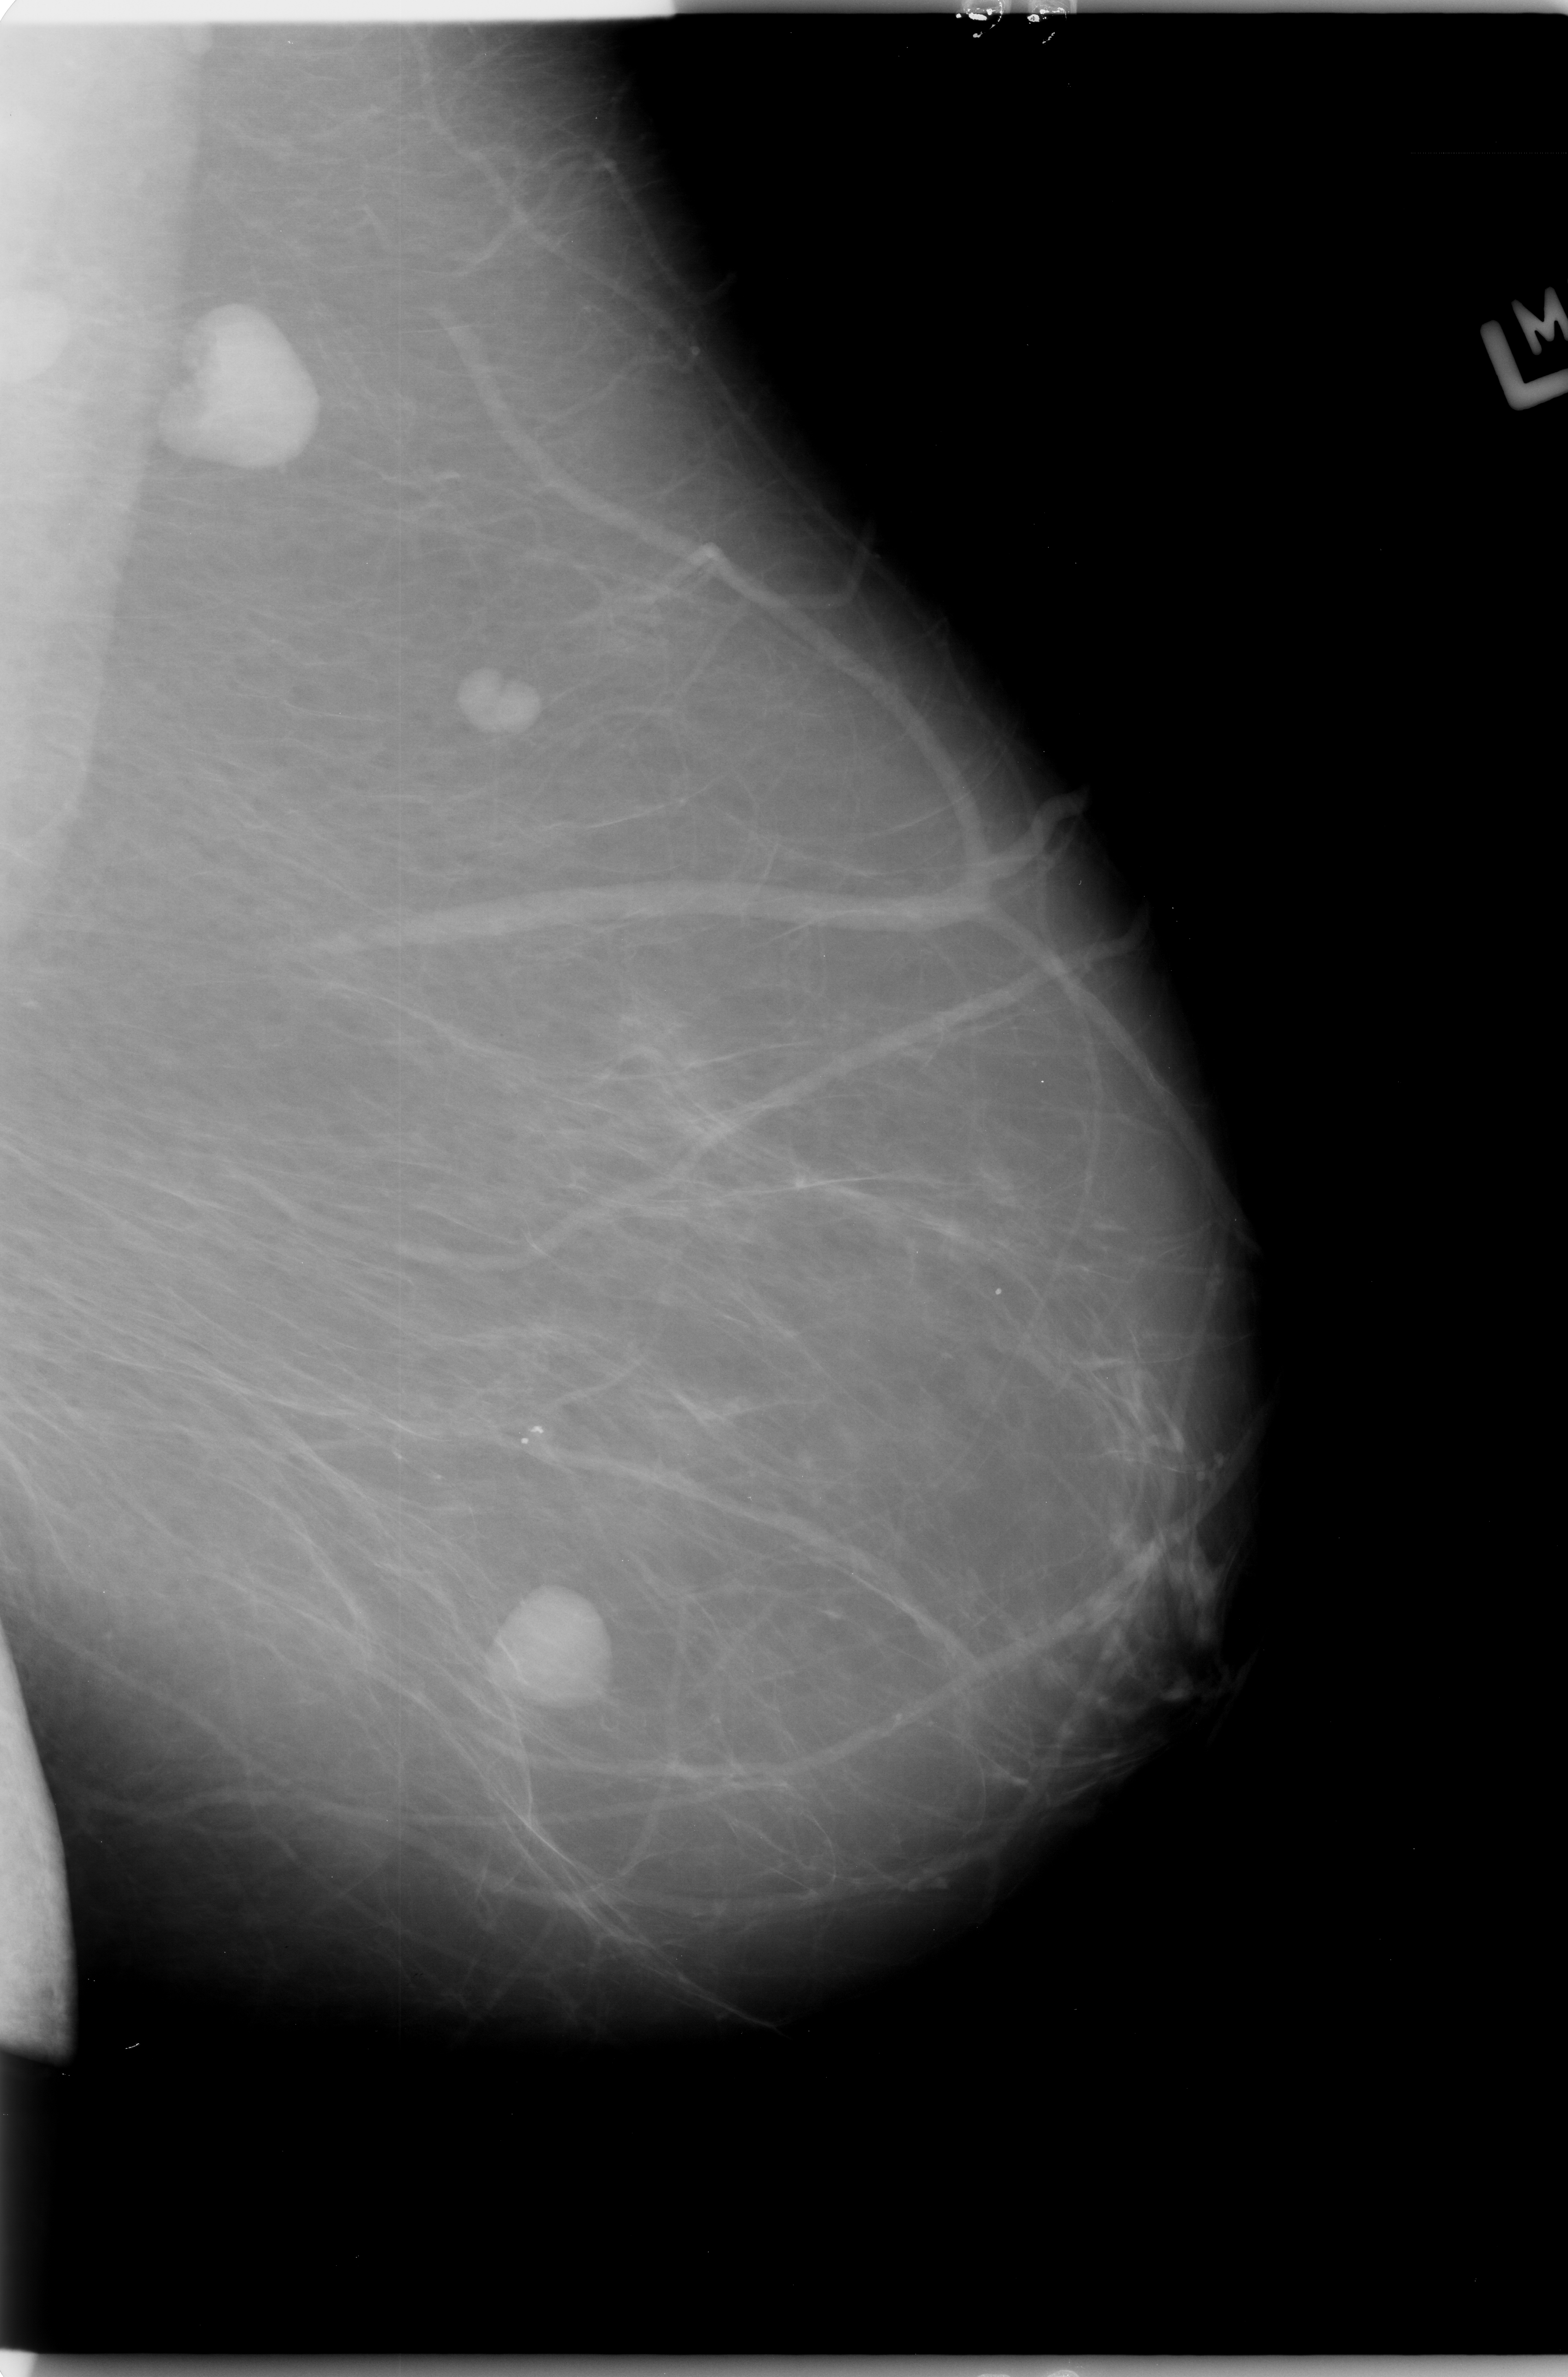
Digitized screen-film mammogram, left breast, mediolateral oblique (MLO) view.
Mass, shape oval, margins circumscribed; BI-RADS assessment category 4; subtlety rating 5 on a 1 (subtle) to 5 (obvious) scale; pathology (as recorded): benign.